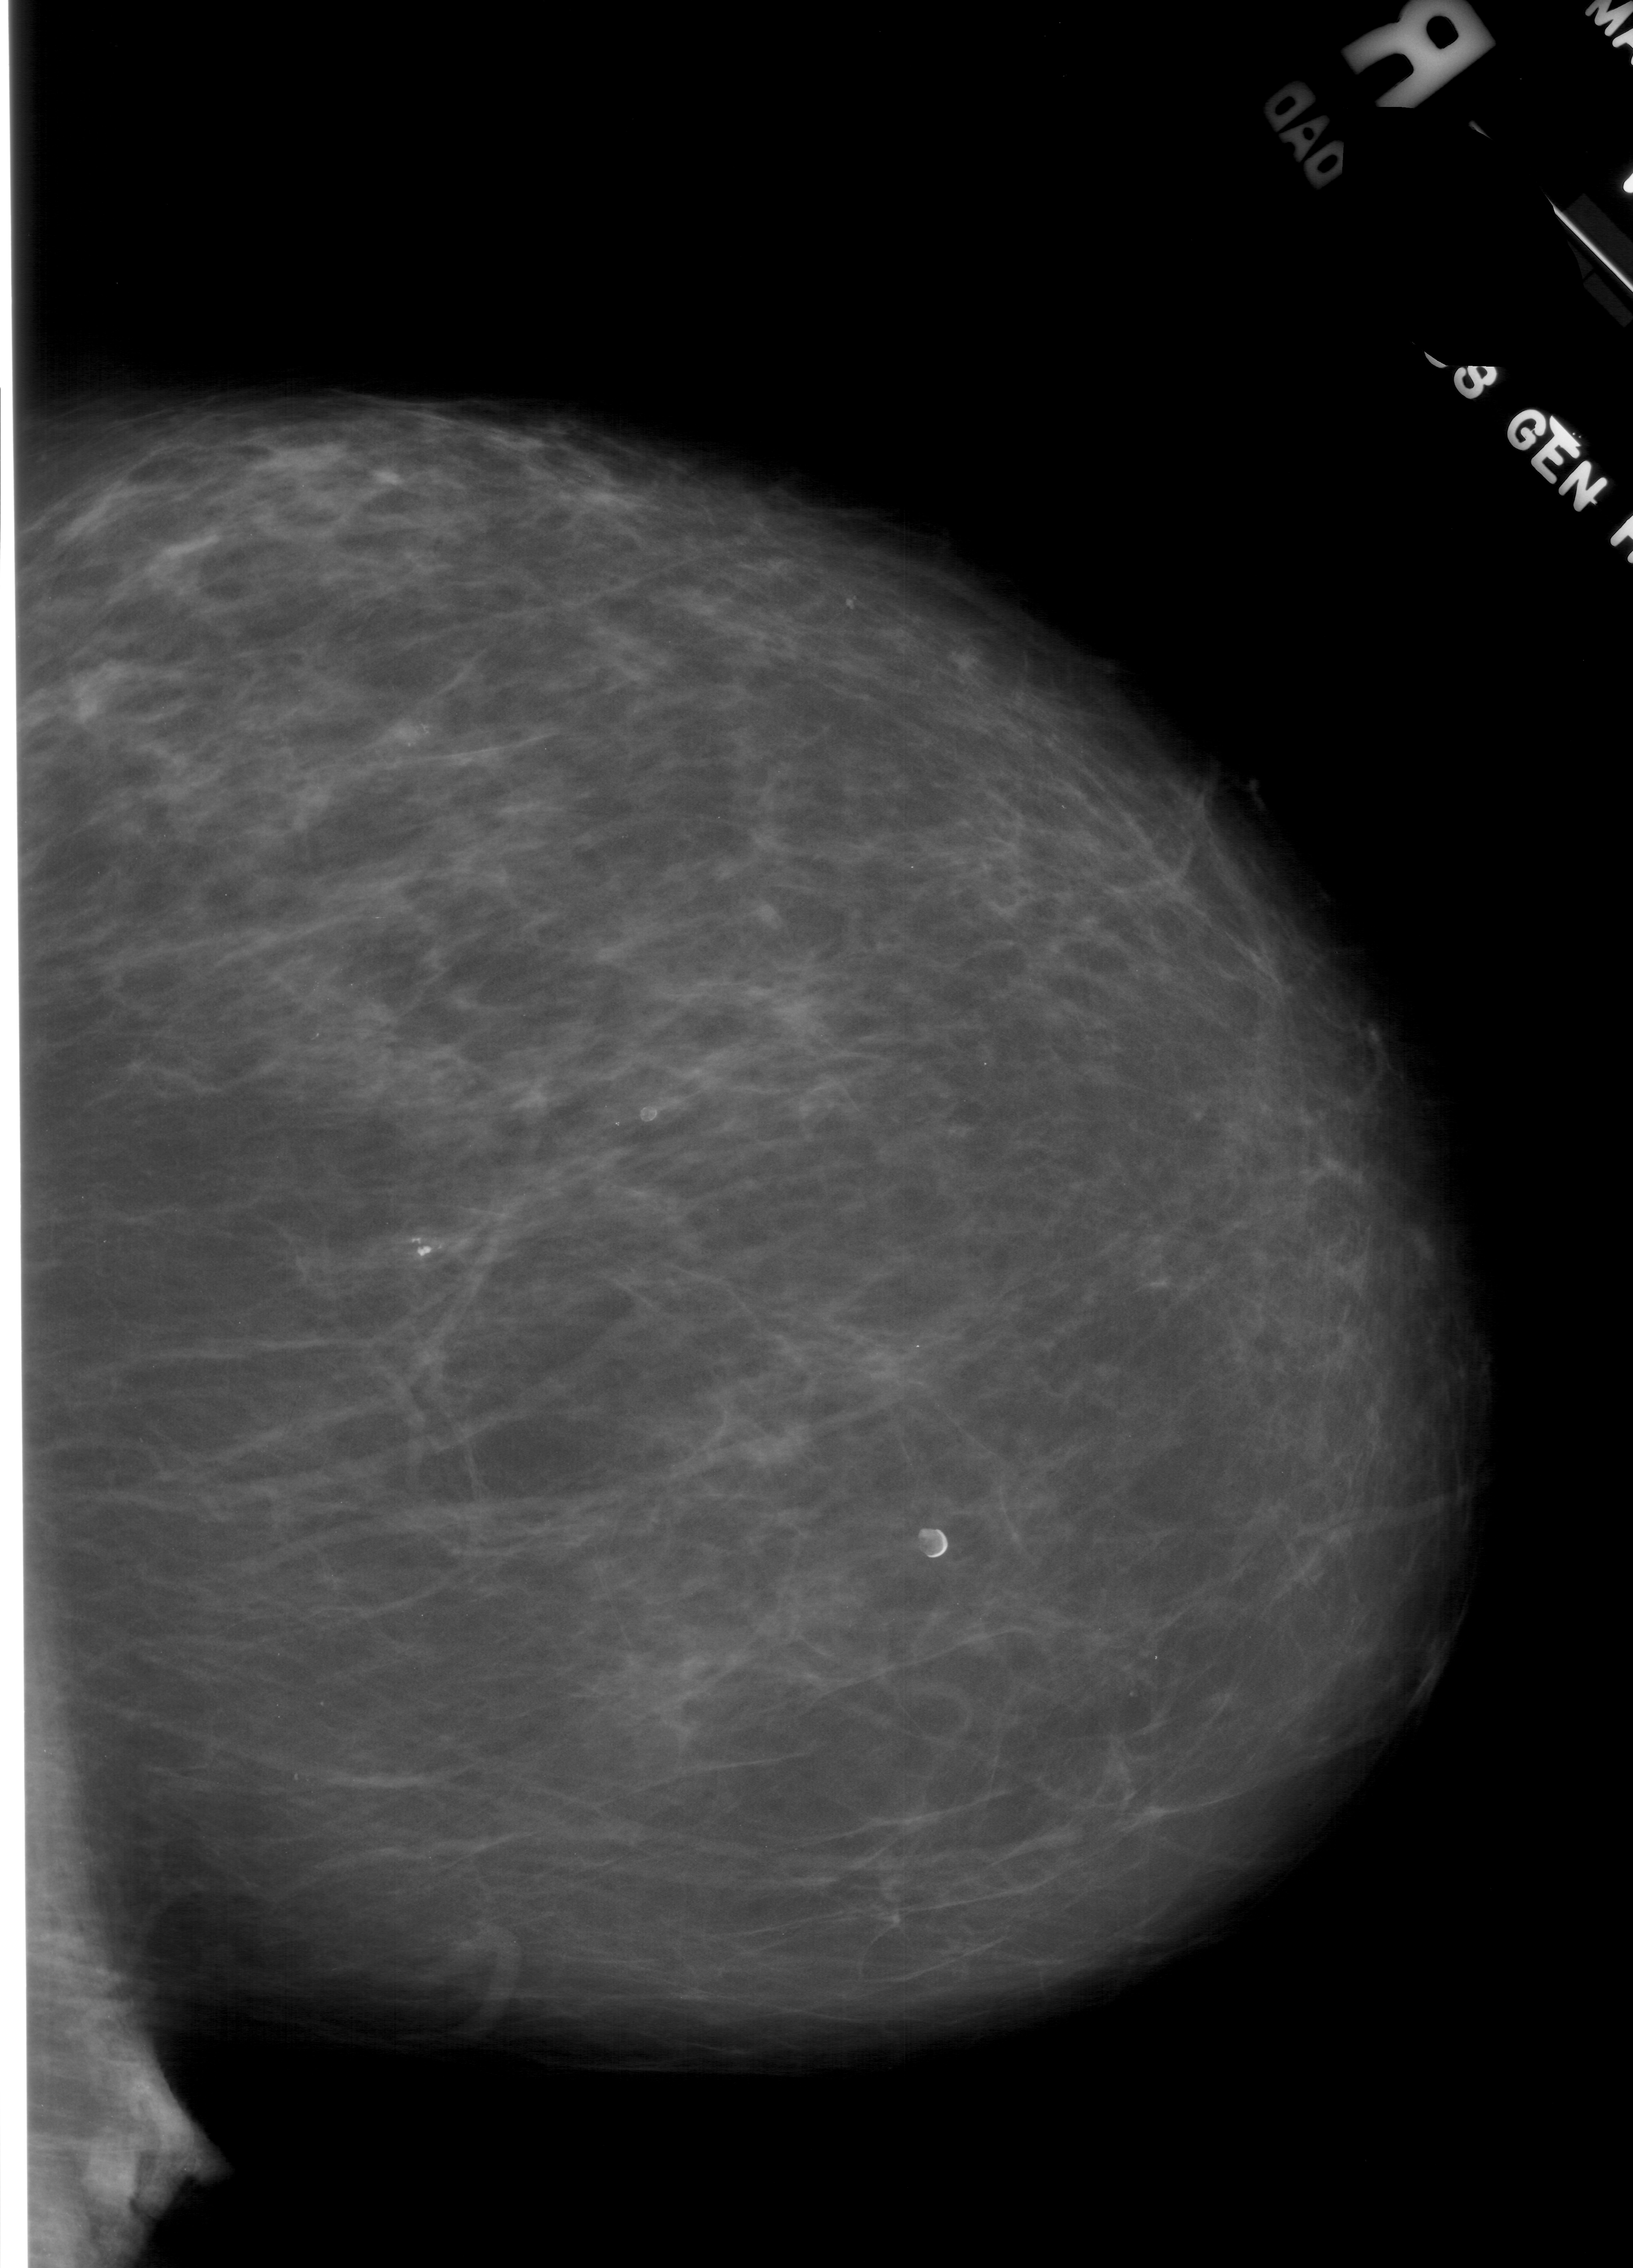
Scanned film-screen mammogram; right breast; CC view; 1633 × 2268 image matrix.
Expert-marked regions of interest on this image (one box per marked abnormality):
- calcifications, morphology pleomorphic, distribution clustered; BI-RADS assessment category 4; subtlety rating 2 on a 1 (subtle) to 5 (obvious) scale; pathology (as recorded): benign: bounding box [x1, y1, x2, y2] px = [666, 1742, 762, 1805]